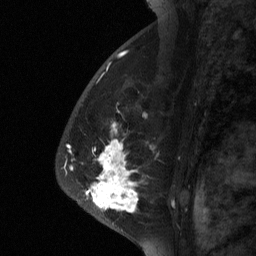
Breast MRI (dynamic contrast-enhanced), one sagittal slice; position 43 of 64 along the scan axis; dynamic contrast-enhanced study with each time point stored as its own series, time point 2 of 3 at this slice position (early post-contrast, ordered by acquisition time); 1.5 T; TE 4.8 ms, TR 27 ms; 256 × 256 image matrix. Patient: female, 56 years. From the clinical record (not read from this slice): setting: breast cancer imaged before/during neoadjuvant chemotherapy; receptor status: HER2-positive.
Annotated regions visible in this slice (semi-automatic segmentation, software-assisted and operator-edited):
- analysis volume of interest (the breast-tissue region the enhancement analysis was run in; not a lesion): box from (x=75, y=104) to (x=182, y=229) px
- tumour enhancement mask (voxels above the 90 % enhancement threshold inside the analysis volume of interest): (x=85, y=123)–(x=138, y=213)